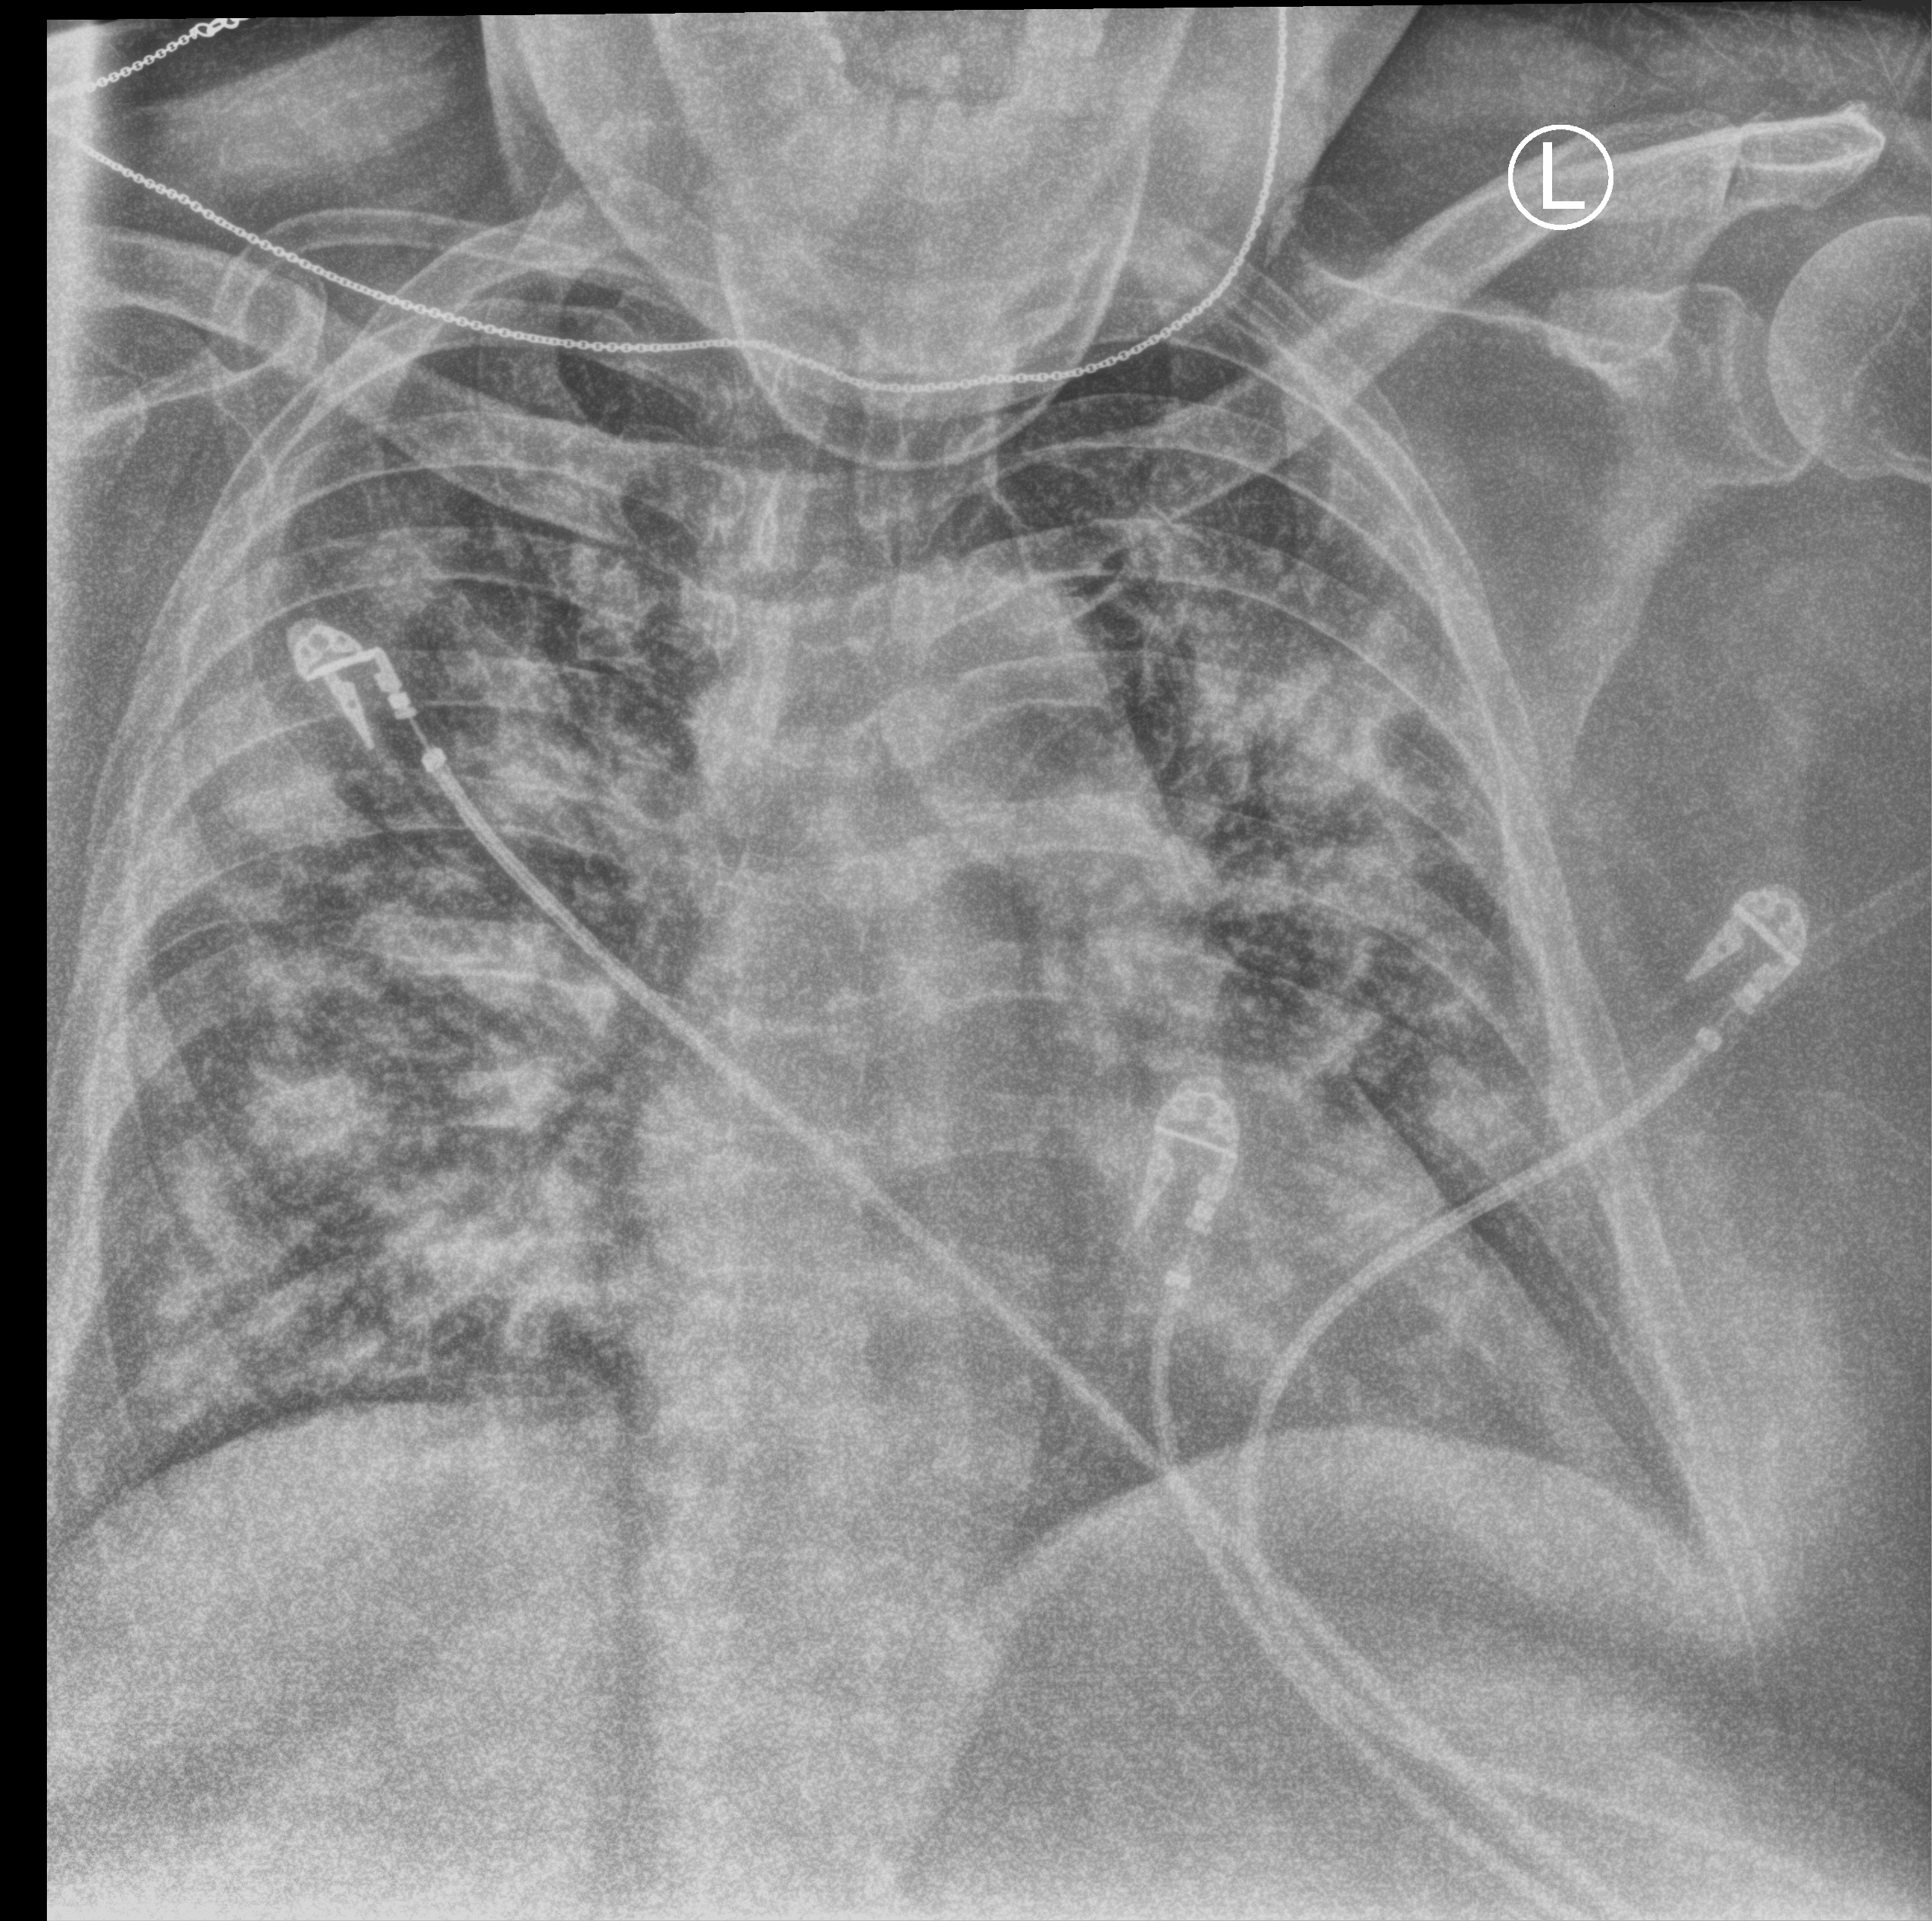
Bedside chest radiograph (computed radiography); anteroposterior (AP) projection. Patient hospitalised with COVID-19; female, aged 60–74 years.
Hospital-stay facts (about this admission, not read from this image; timing relative to this image not recorded):
- admitted to intensive care during this hospital stay: no